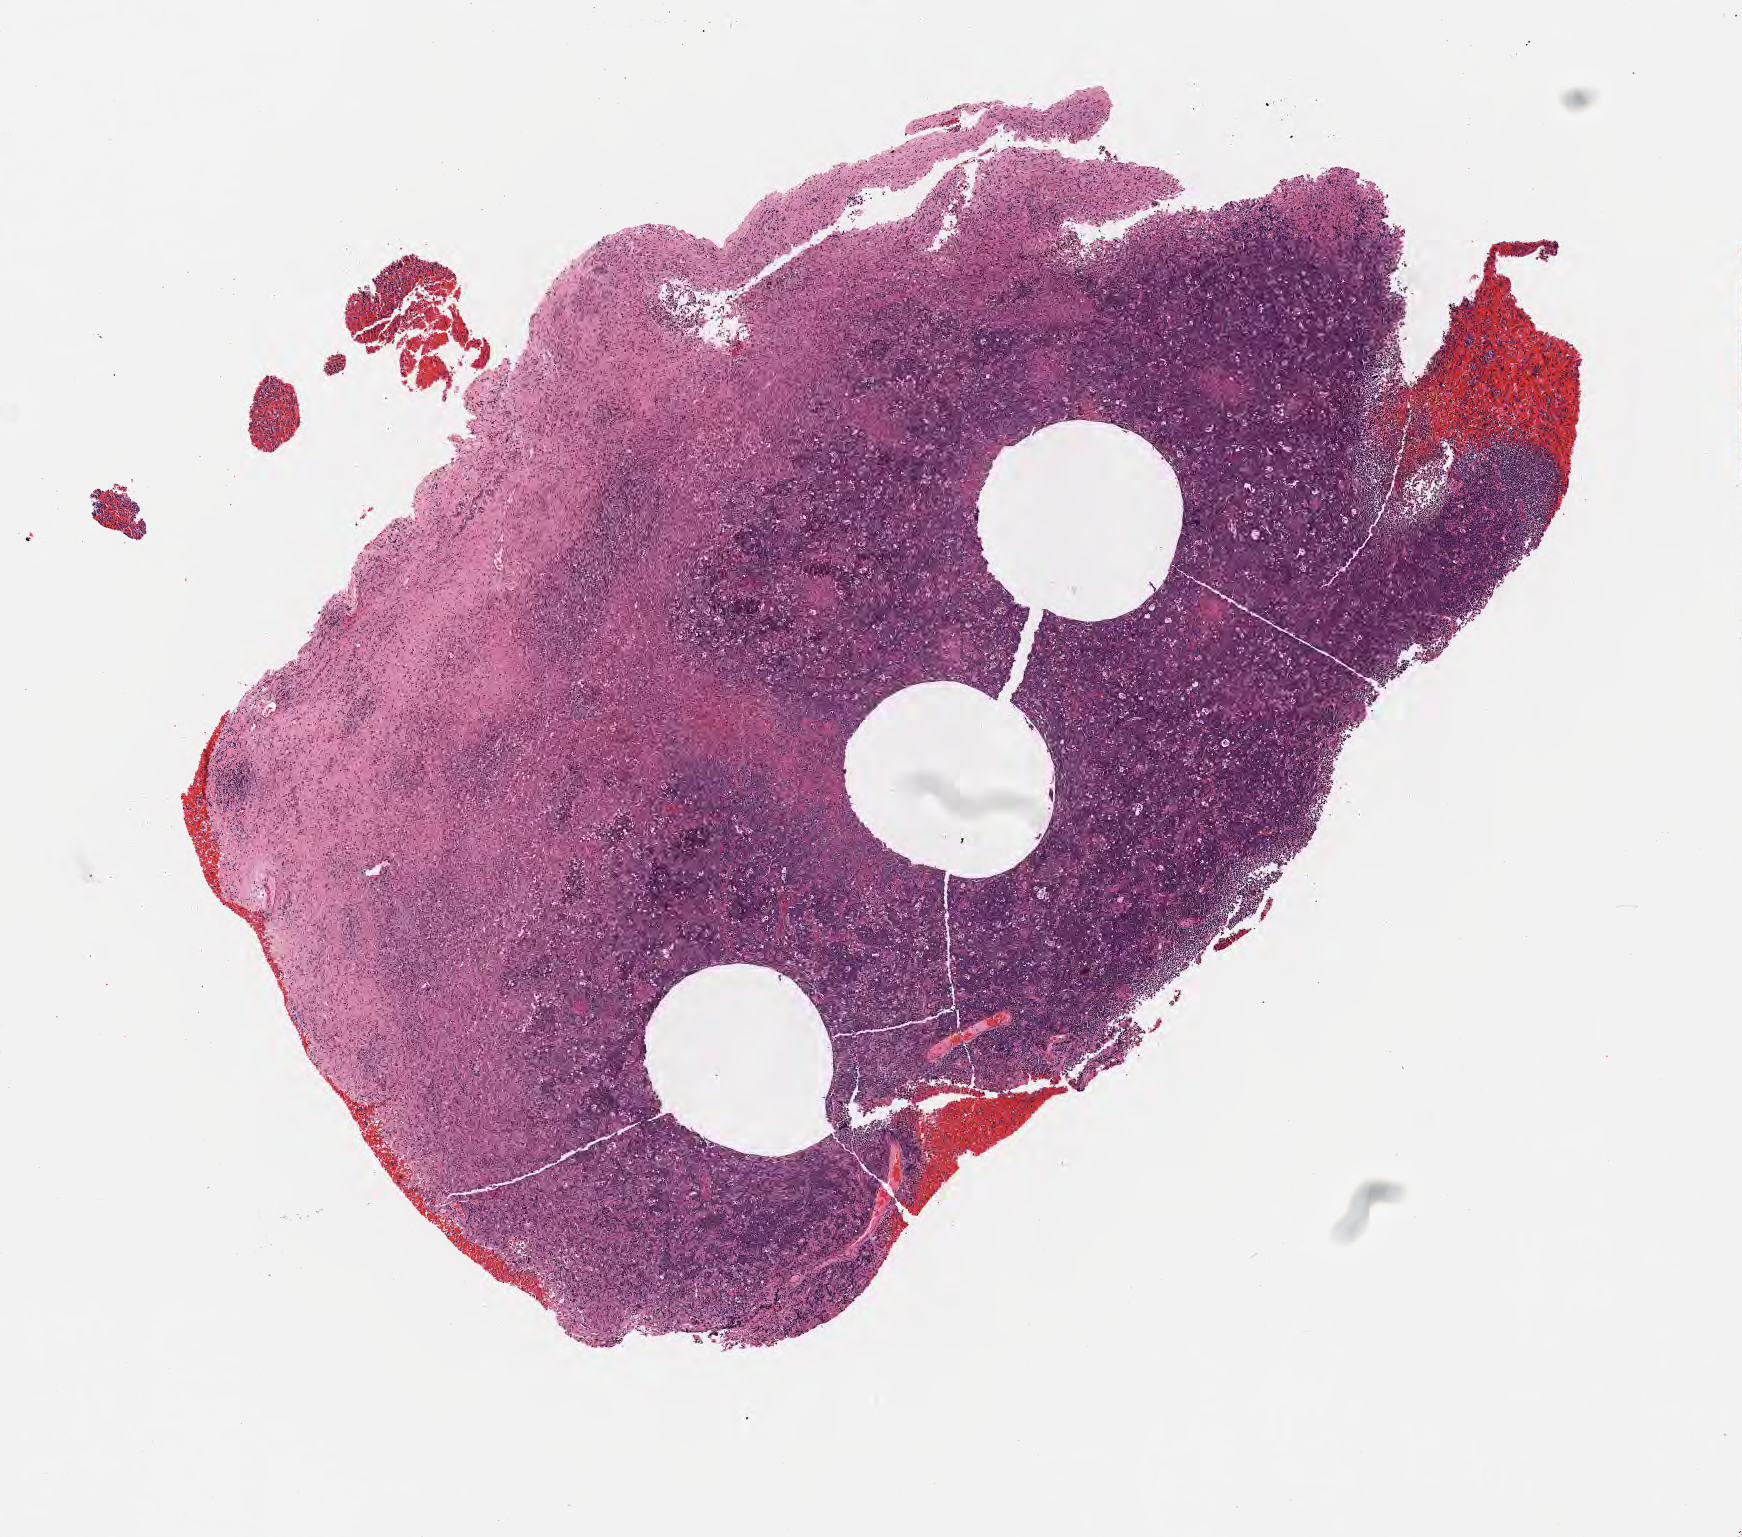
Digitized haematoxylin and eosin-stained section — shown as a low-resolution overview of the whole scanned area (about 7.0 x 6.2 mm). FFPE section. Specimen: primary tumor. Site: lymph node of head and neck. Male patient; age at initial diagnosis 5 years. Composition of this section per pathologist review: tumor cells 60%, tumor nuclei 80%, stromal cells 15%, necrosis 15%, normal cells 10%. Inflammatory infiltration, as recorded: lymphocyte infiltration 30%, monocyte infiltration 30%, neutrophil infiltration 10%.
Diagnosis: Burkitt lymphoma, NOS. Ann Arbor stage (patient): Stage I. Section: top of the tissue portion.